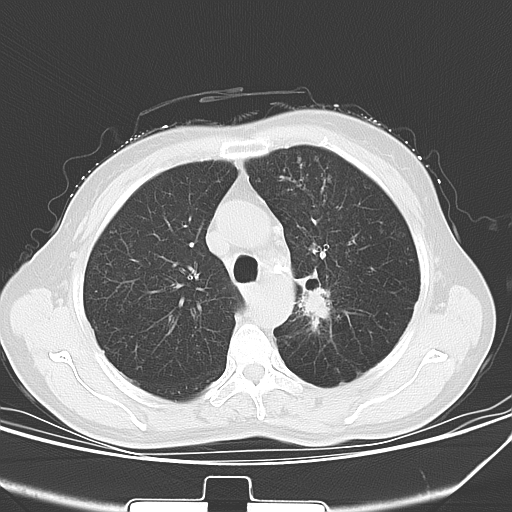
Chest CT, one axial slice. Position 41 of 53 along the scan axis. 120 kVp. Lung window (W 1500 / L -600 HU). 512 × 512 image matrix, field of view 329 × 329 mm. Patient: female, 60 years. Case-level facts recorded for this patient, not image findings: clinical TNM (as recorded): T1b N0 M0.
Annotated regions visible in this slice (rectangle marked by the reading radiologist):
- lung tumour (recorded histology: squamous cell carcinoma): bounding box (x1, y1, x2, y2) in pixels: (293, 265, 340, 333)